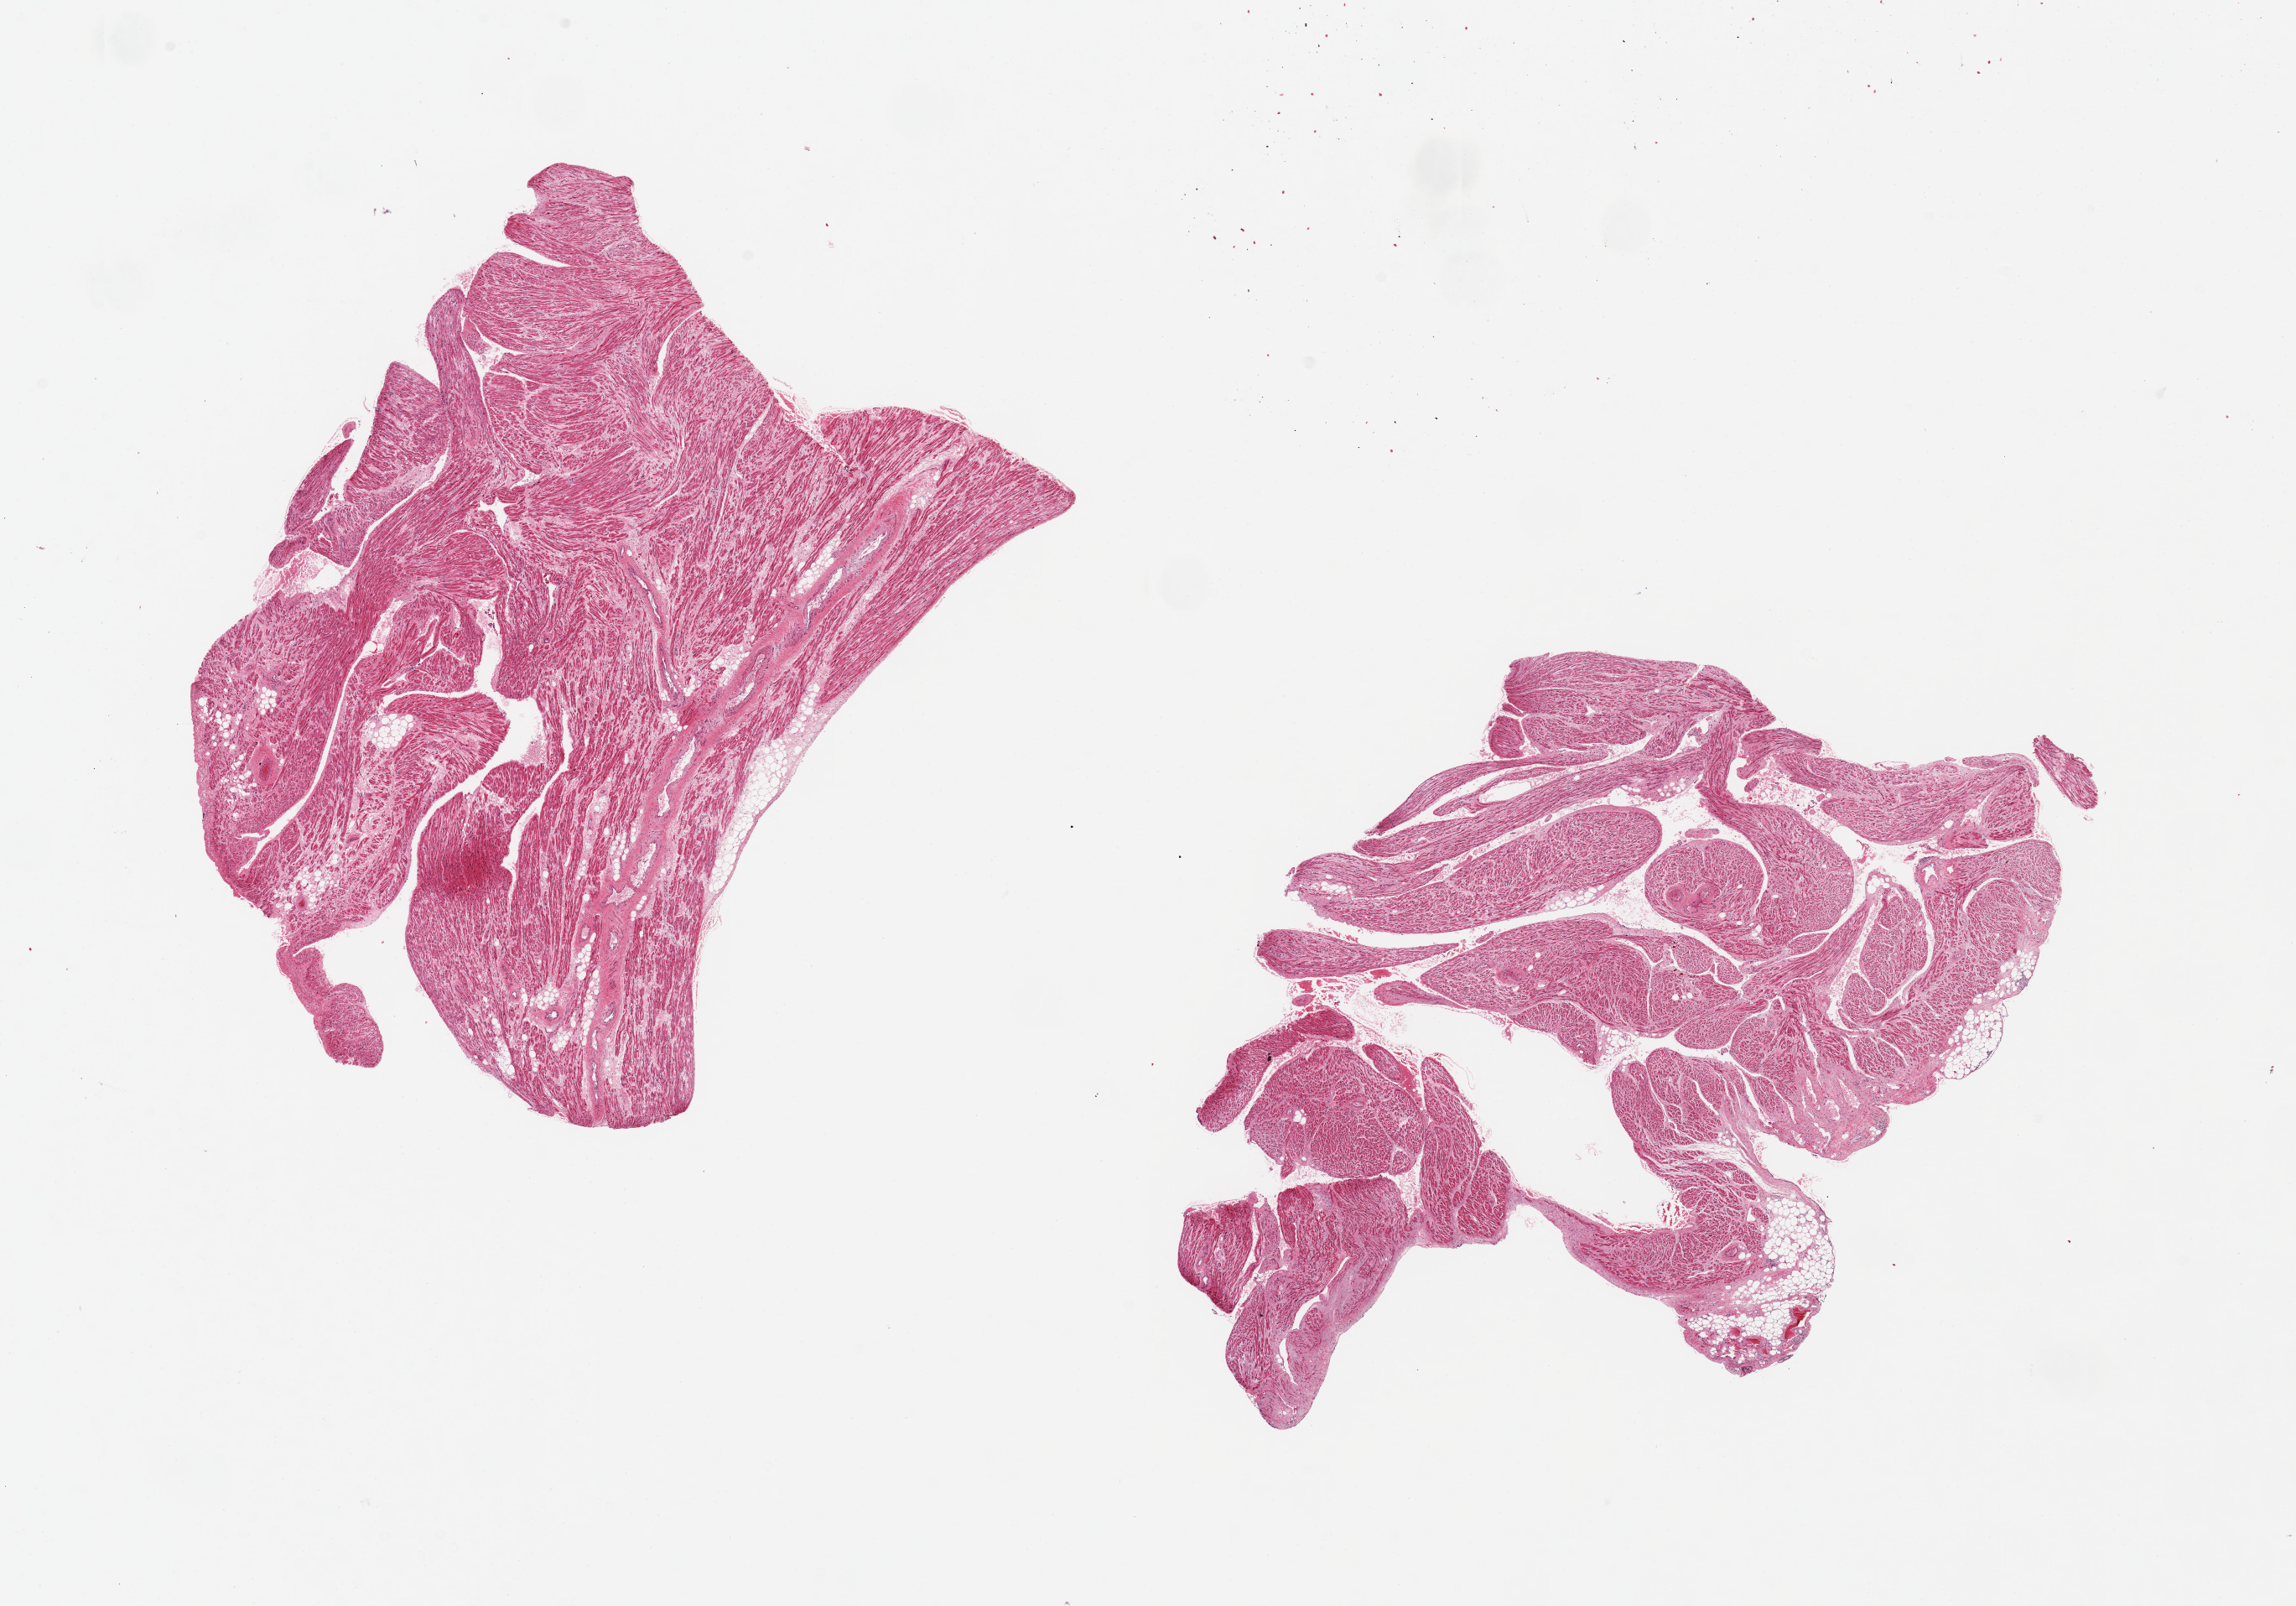
Hematoxylin and eosin (H&E) whole-slide image, brightfield, a low-resolution overview of the entire scanned area, about 21.7 x 15.1 mm (slide scanned at 20x); PAXgene-fixed, paraffin-embedded tissue; section of auricular appendage (target tissue); tissue donor sample. Donor: female.
Review note (as recorded): 2 pieces, 9x6 & 8x6.5mm; well dissected with minimal extraneous adipose.